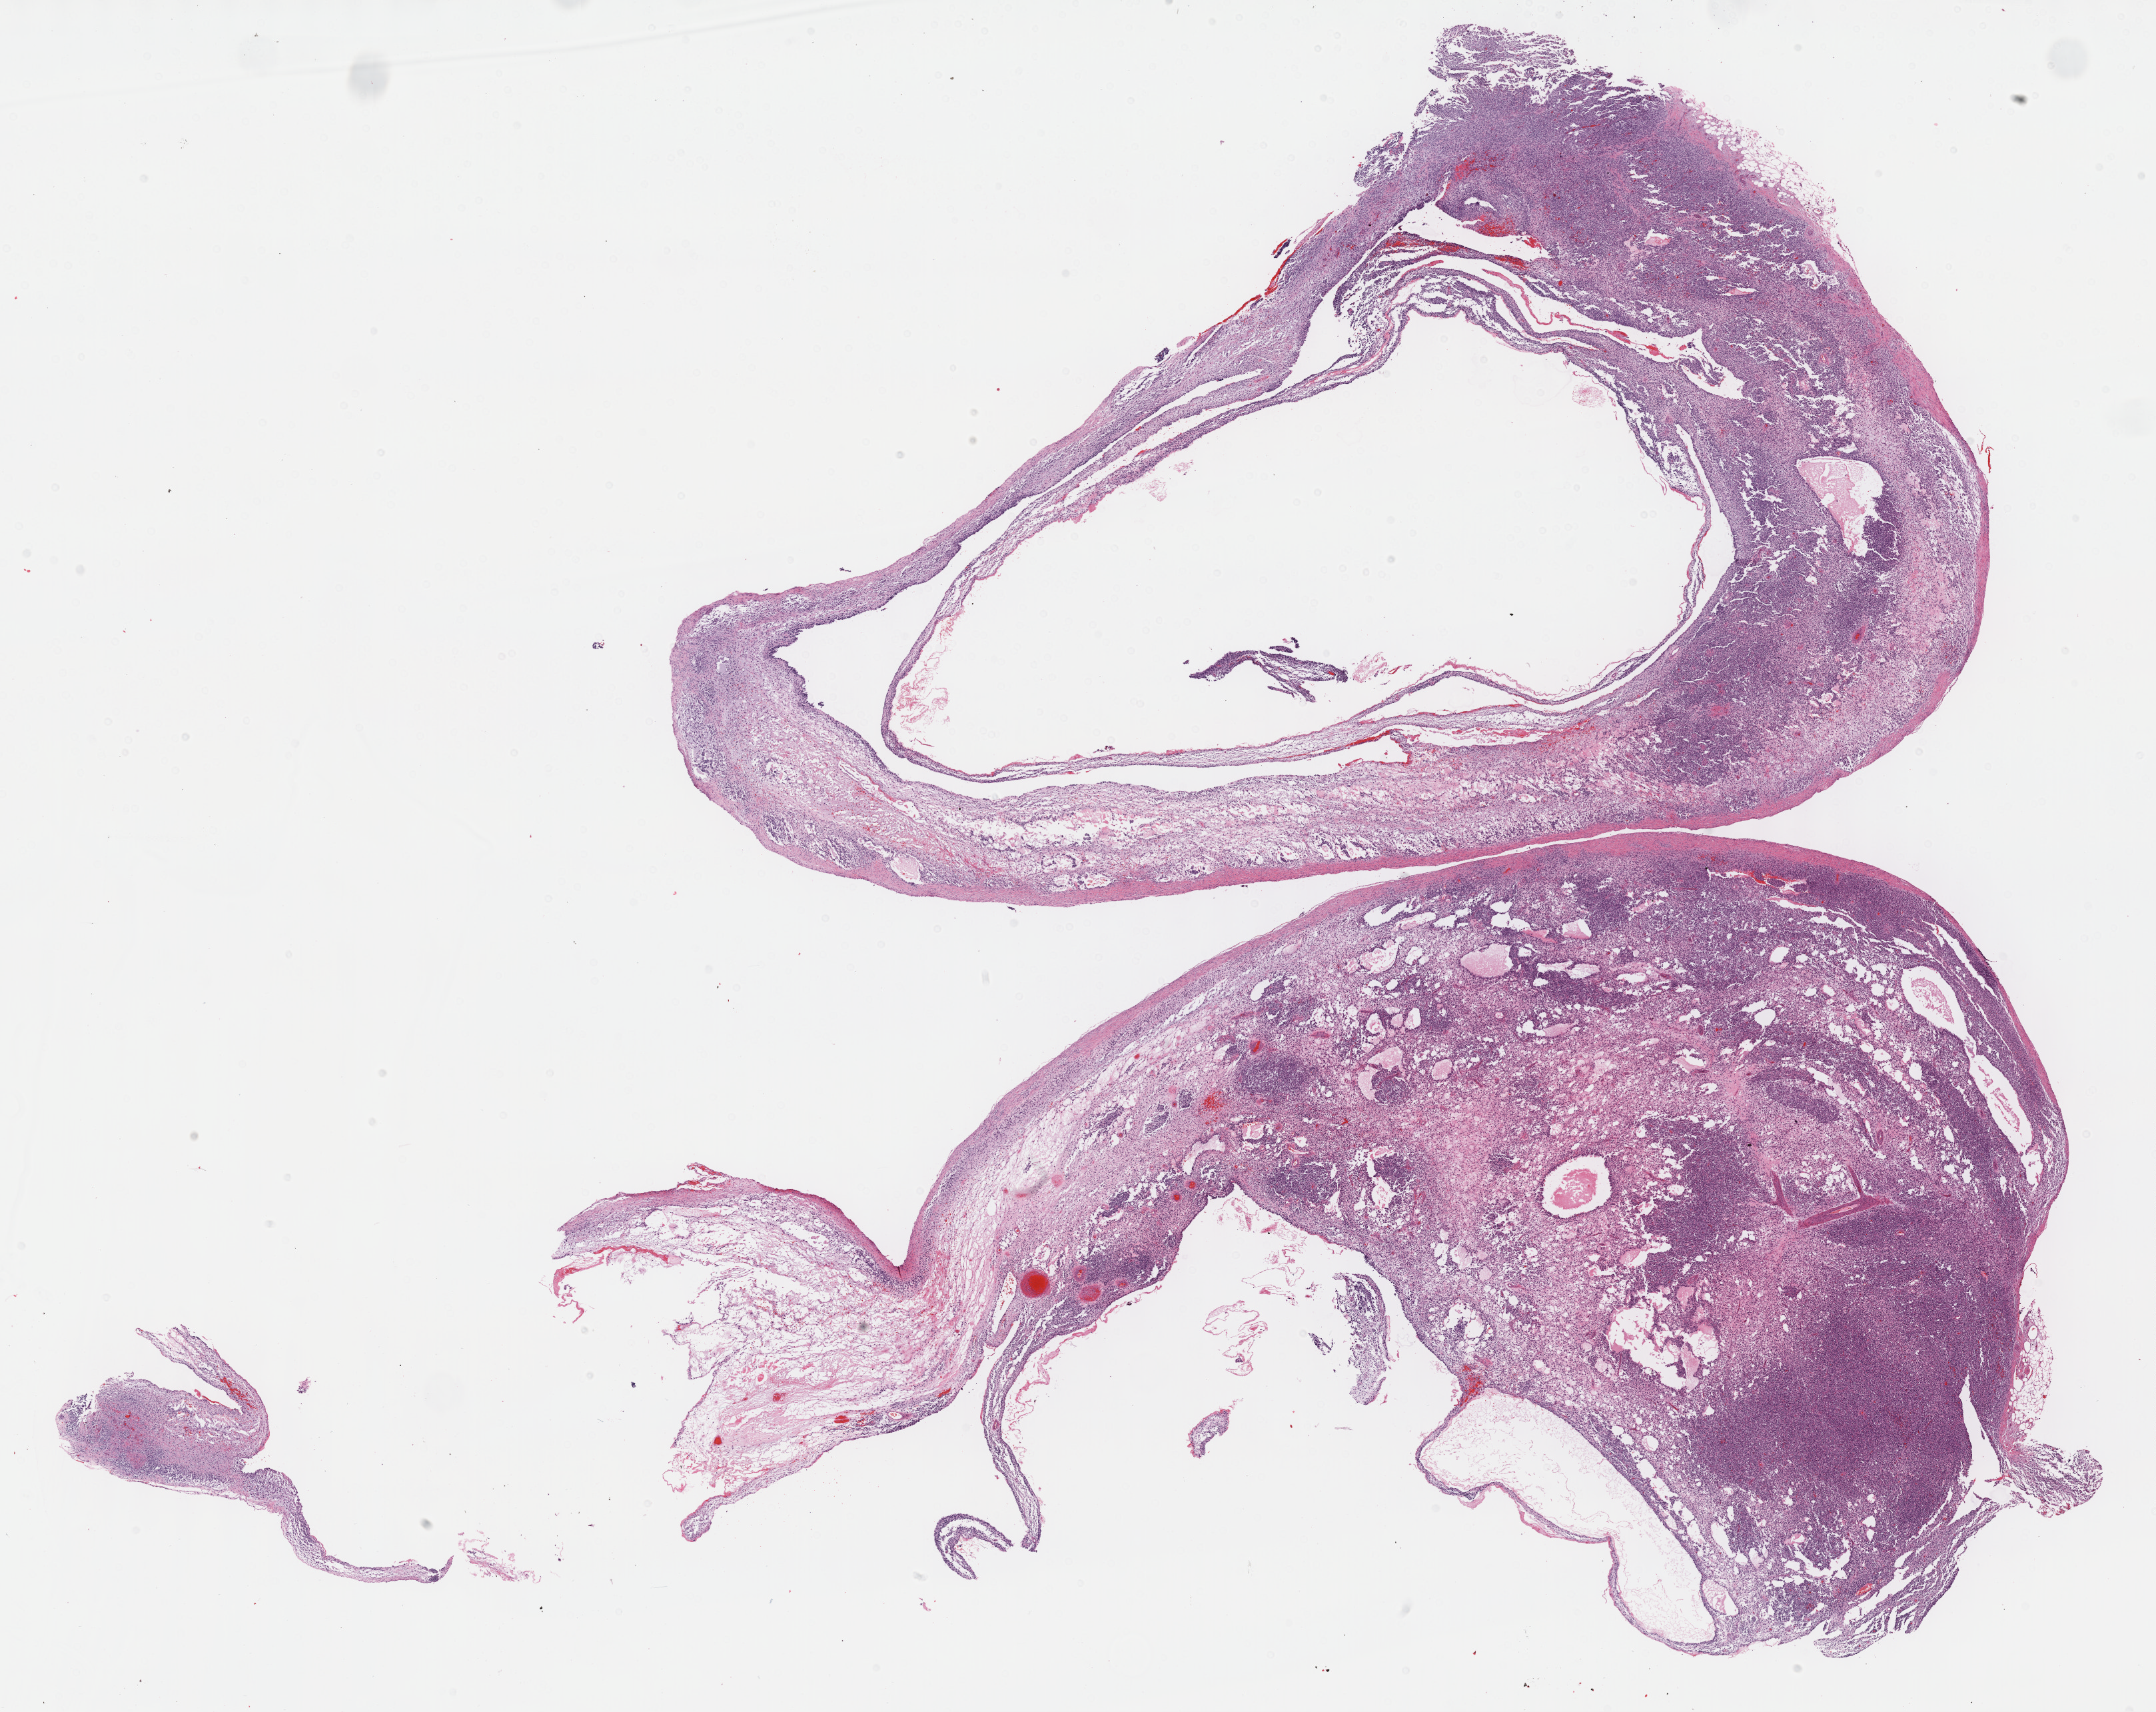
Digitized H&E-stained tissue section (whole slide), a low-resolution overview of the entire scanned area, about 26.2 x 20.8 mm; formalin-fixed paraffin-embedded (FFPE) diagnostic section; sample: primary tumour, retroperitoneum and peritoneum. Male, age 57 years at initial diagnosis.
Pathologic diagnosis: Dedifferentiated liposarcoma.